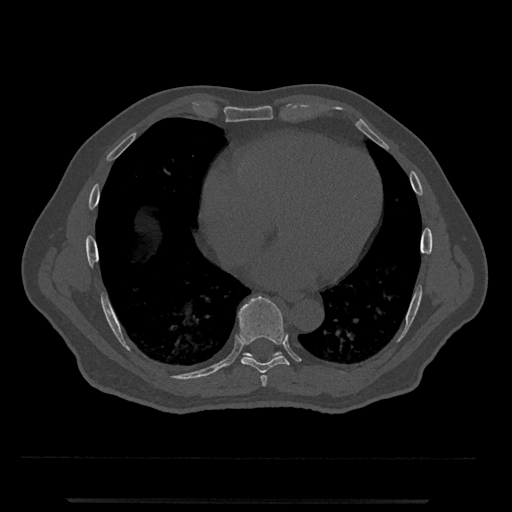
CT including the spine, one axial slice. Position 618 of 797 along the scan axis. 120 kVp. Bone window (W 1800 / L 400 HU). 512 × 512 image matrix. Male patient, age 63 years. From the clinical record (not read from this slice): primary cancer: prostate.
Structures marked on this image (semi-automatic segmentation, software-assisted and operator-edited):
- T7 vertebra: bounding box [x1, y1, x2, y2] px = [260, 375, 267, 387]
- T8 vertebra: [238, 295, 289, 374]
- T9 vertebra: [243, 351, 282, 362]